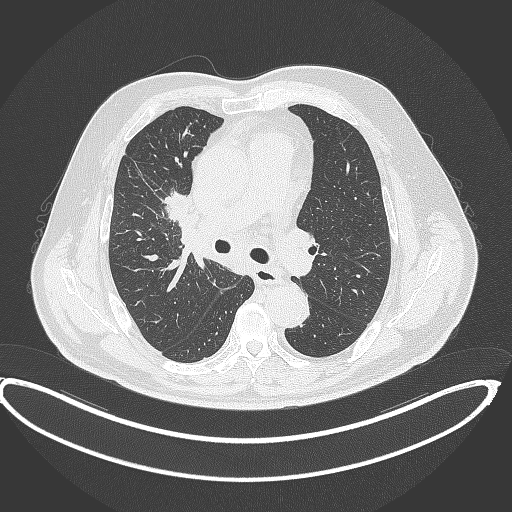
Chest CT, one axial slice. Position 251 of 390 along the scan axis. Reconstruction kernel B70f. 120 kVp. Lung window (W 1500 / L -600 HU). 512 × 512 image matrix. Patient: male, 62 years. From the clinical record (not read from this slice): clinical TNM (as recorded): T1c N3 M1c.
Structures marked on this image (rectangle marked by the reading radiologist):
- lung tumour (recorded histology: adenocarcinoma): box from (x=160, y=186) to (x=193, y=223) px